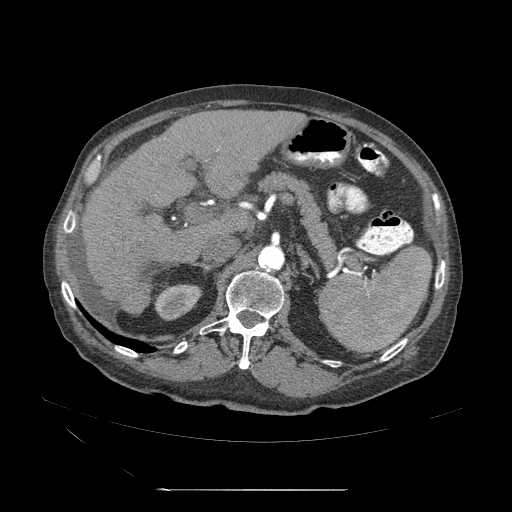
Contrast-enhanced abdominal CT (liver protocol), one axial slice. Slice 25 of 71 in the series (ordered by position). 120 kVp. Soft-tissue window (W 400 / L 40 HU). 2.5 mm slice thickness. 512 × 512 image matrix, field of view 440 × 440 mm. Case-level facts recorded for this patient, not image findings: diagnosis: hepatocellular carcinoma (patient treated with transarterial chemoembolisation; whether this scan precedes or follows treatment is not stated here); TNM stage (as recorded): Stage-II; Child-Pugh class: A; tumour nodularity: multinodular; tumour size: 1 cm.
Structures marked on this image (semi-automatic segmentation, software-assisted and operator-edited):
- abdominal aorta: bounding box (x1, y1, x2, y2) in pixels: (259, 244, 286, 272)
- liver parenchyma outside the tumour (the mass and vessels are separate outlines, so this box may not span the whole liver): (82, 113, 293, 317)
- liver vessels: (146, 159, 240, 265)